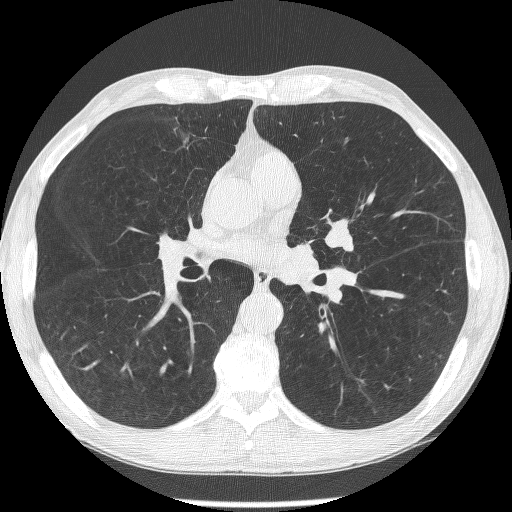
Axial slice from a low-dose chest CT screening exam. Second annual screen. Lung window (W 1500 / L -600 HU). 1.25 mm slice thickness. Slice 144 of 293 in the series. 512 × 512 image matrix. Male, age 62 years at enrolment. Former smoker at enrolment.
Expert-annotated lung lesion, bounding box [x1, y1, x2, y2] px = [318, 217, 368, 265]. The screening reader recorded 2 non-calcified nodules or masses ≥4 mm on this exam (lingula, lingula); which of them this box marks is not recorded. Later outcome: lung cancer diagnosed 95 days after this screen — small cell carcinoma, NOS, left upper lobe, stage IIIA (AJCC 6th edition).